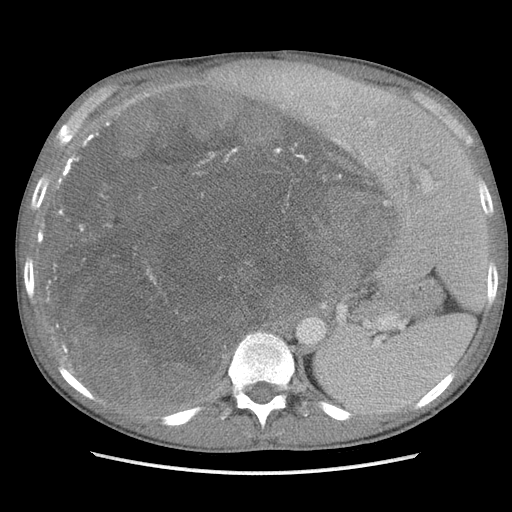
Contrast-enhanced abdominal CT, one axial slice. Slice 75 of 115 in the series (ordered by position). Soft-tissue window (W 400 / L 40 HU). 5 mm slice thickness. 512 × 512 image matrix. Male patient. From the clinical record (not read from this slice): diagnosis: adrenocortical carcinoma; tumour side: right adrenal; Ki-67 index: 13 %; stage (as recorded): 3.
Structures marked on this image (semi-automatically segmented with operator editing):
- mass: bounding box <50,91,388,412> (left, top, right, bottom; pixels)